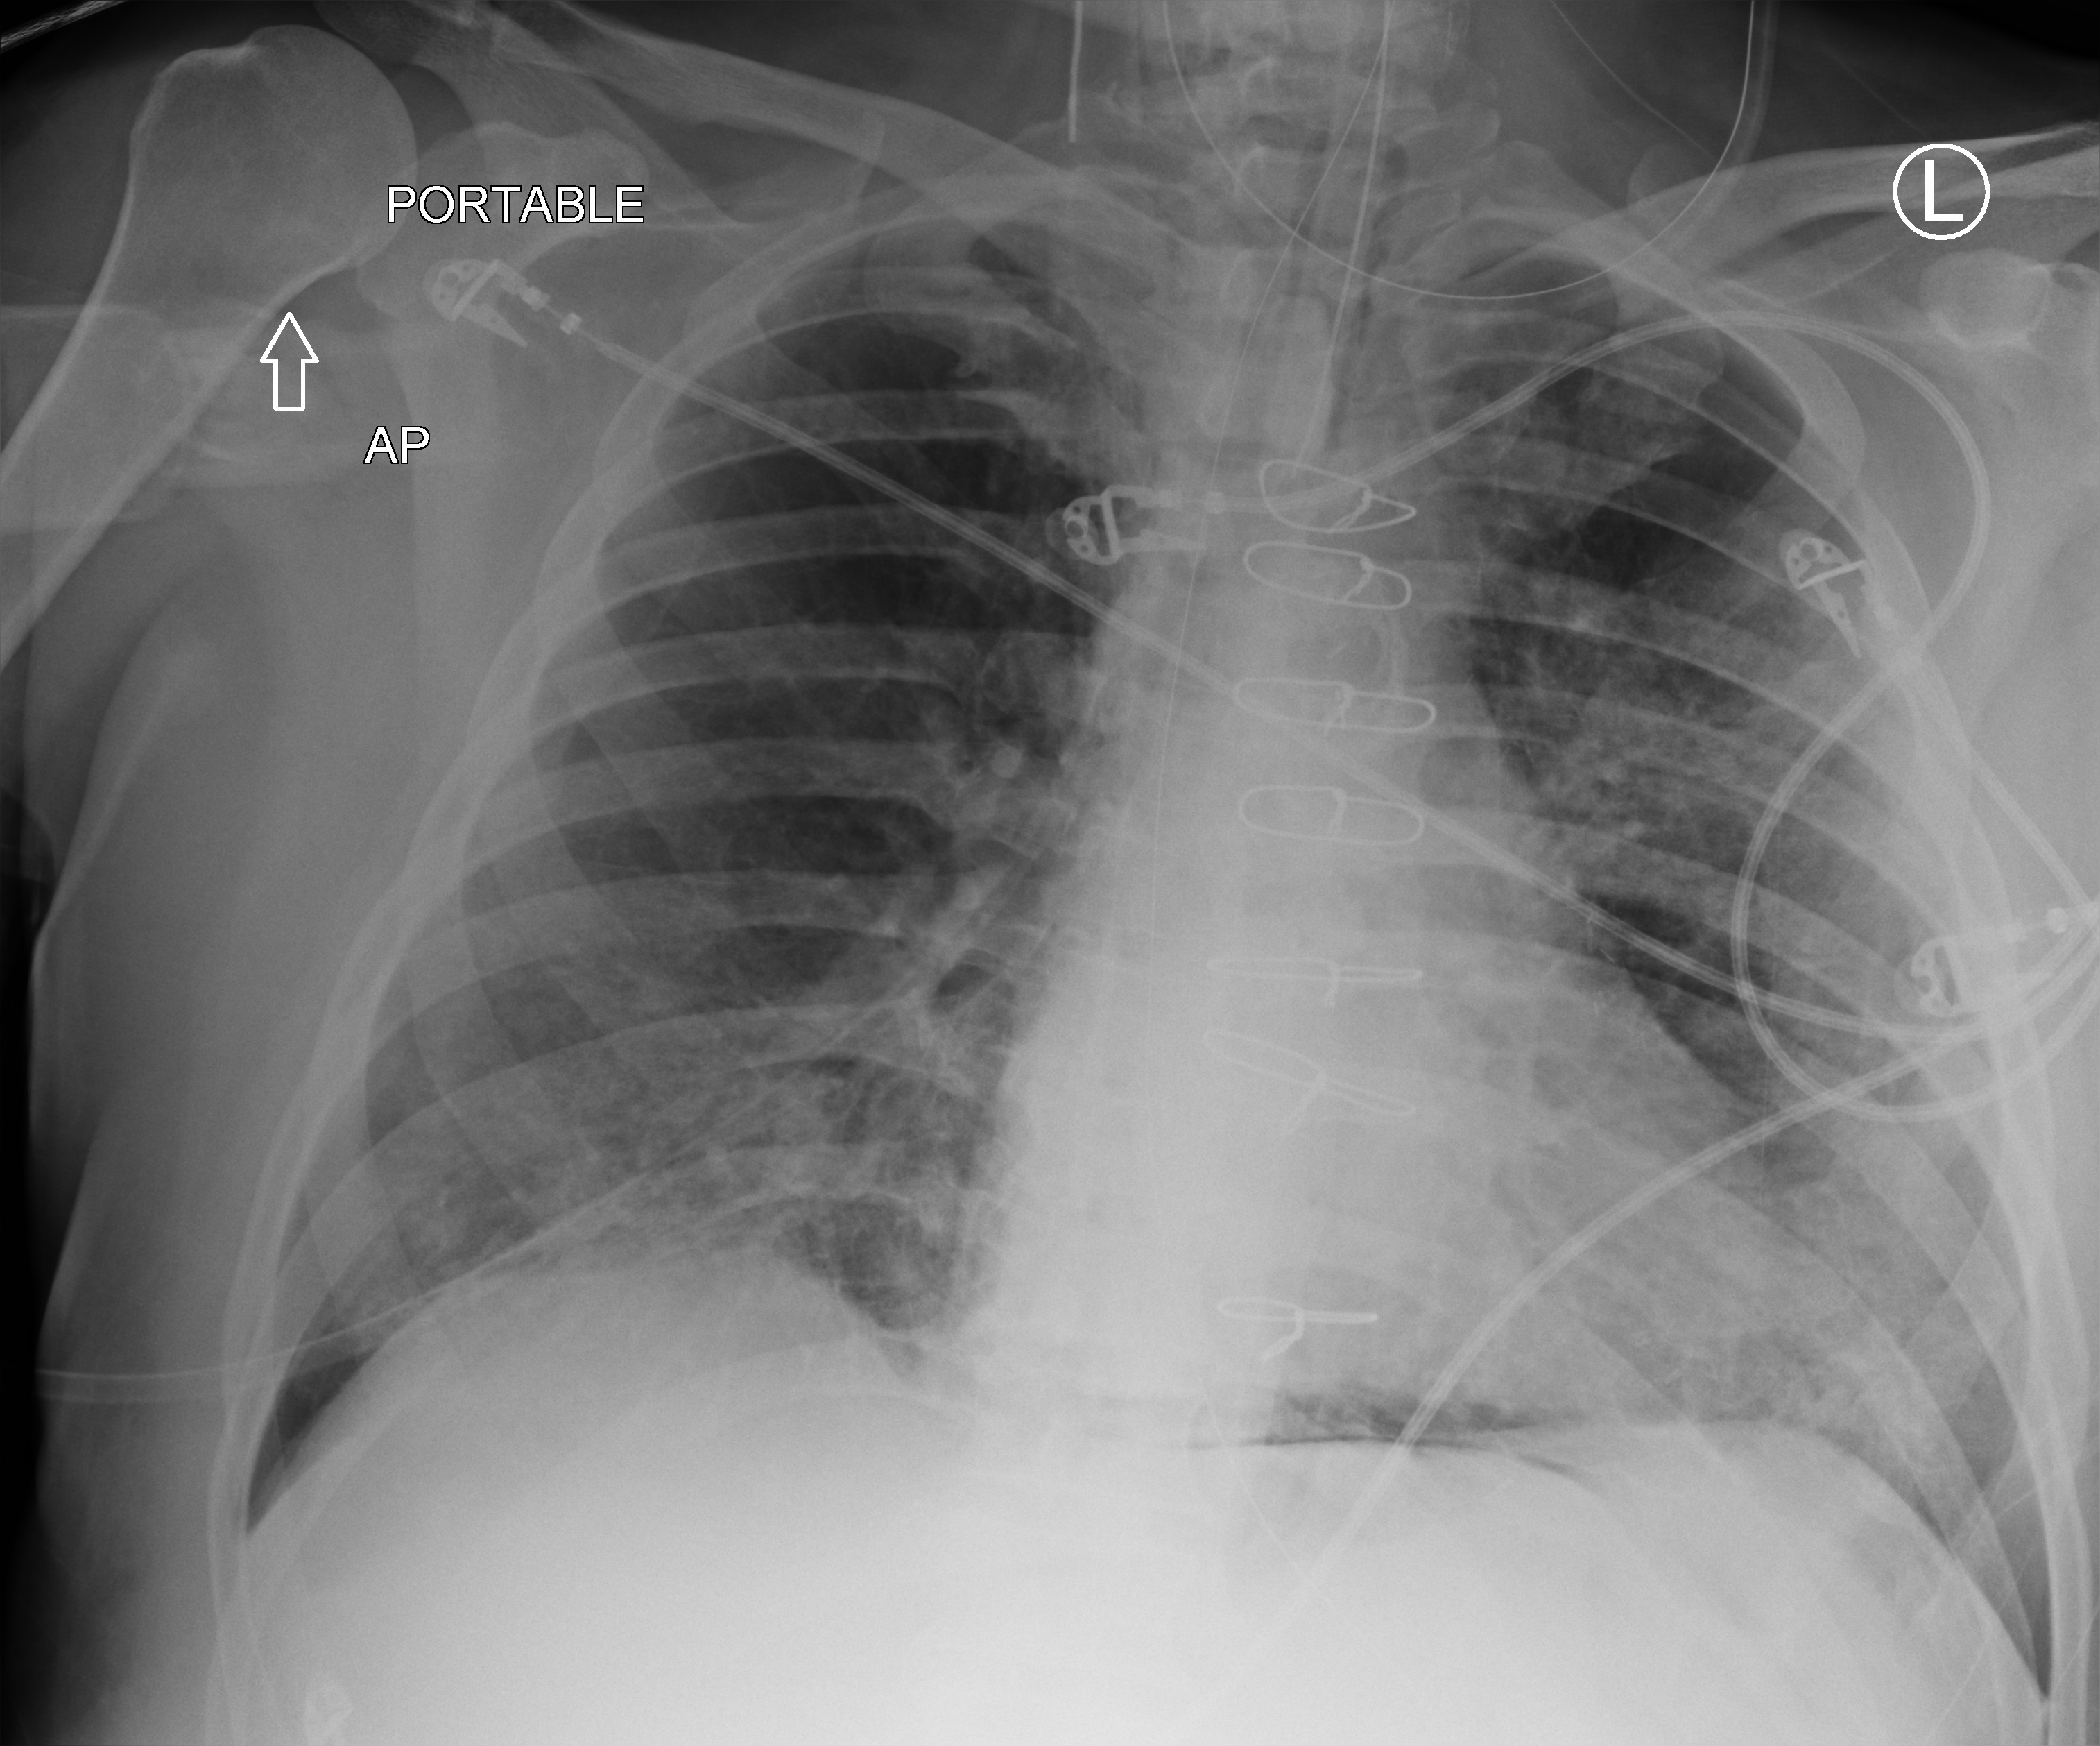
Chest X-ray (portable). Patient hospitalised with COVID-19; male, aged 60–74 years.
From the hospital-stay record, not from the radiograph (when in the stay this image was taken is not recorded):
- other chronic lung disease (admission record): no
- smoking status (admission record): former